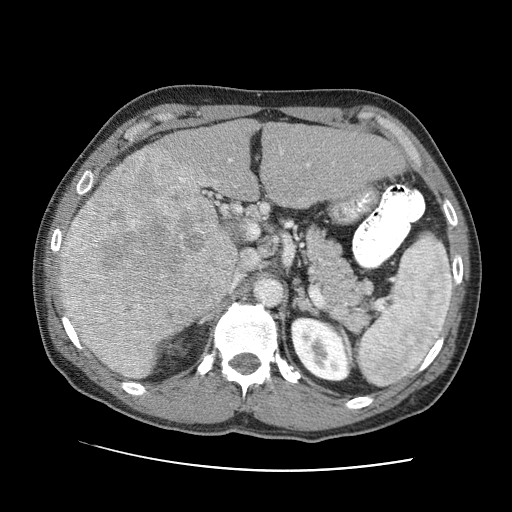
Contrast-enhanced abdominal CT (liver protocol), one axial slice; slice 49 of 95 in the series (ordered by position); reconstruction kernel STANDARD; 120 kVp; one of 2 acquisitions stored at this slice position; soft-tissue window (W 400 / L 40 HU); 512 × 512 image matrix. Case-level facts recorded for this patient, not image findings: diagnosis: hepatocellular carcinoma (patient treated with transarterial chemoembolisation; whether this scan precedes or follows treatment is not stated here); TNM stage (as recorded): Stage-IVA; Child-Pugh class: A; tumour differentiation: moderately differentiated; tumour nodularity: multinodular.
Structures marked on this image (semi-automatically segmented with operator editing):
- abdominal aorta: bounding box (x1, y1, x2, y2) in pixels: (255, 279, 282, 306)
- liver parenchyma outside the tumour (the mass and vessels are separate outlines, so this box may not span the whole liver): (58, 120, 404, 378)
- mass: (59, 144, 238, 378)
- liver vessels: (199, 150, 310, 290)